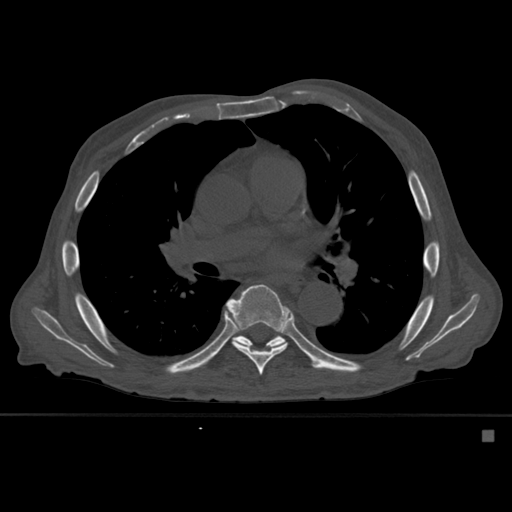
CT including the spine, one axial slice. Position 363 of 527 along the scan axis. Bone window (W 1800 / L 400 HU). 512 × 512 image matrix, field of view 373 × 373 mm. Patient: male, 78 years. From the clinical record (not read from this slice): primary cancer: prostate.
Structures marked on this image (semi-automatic segmentation, software-assisted and operator-edited):
- T7 vertebra: bounding box <225,284,293,375> (left, top, right, bottom; pixels)
- T8 vertebra: <234,332,285,347>